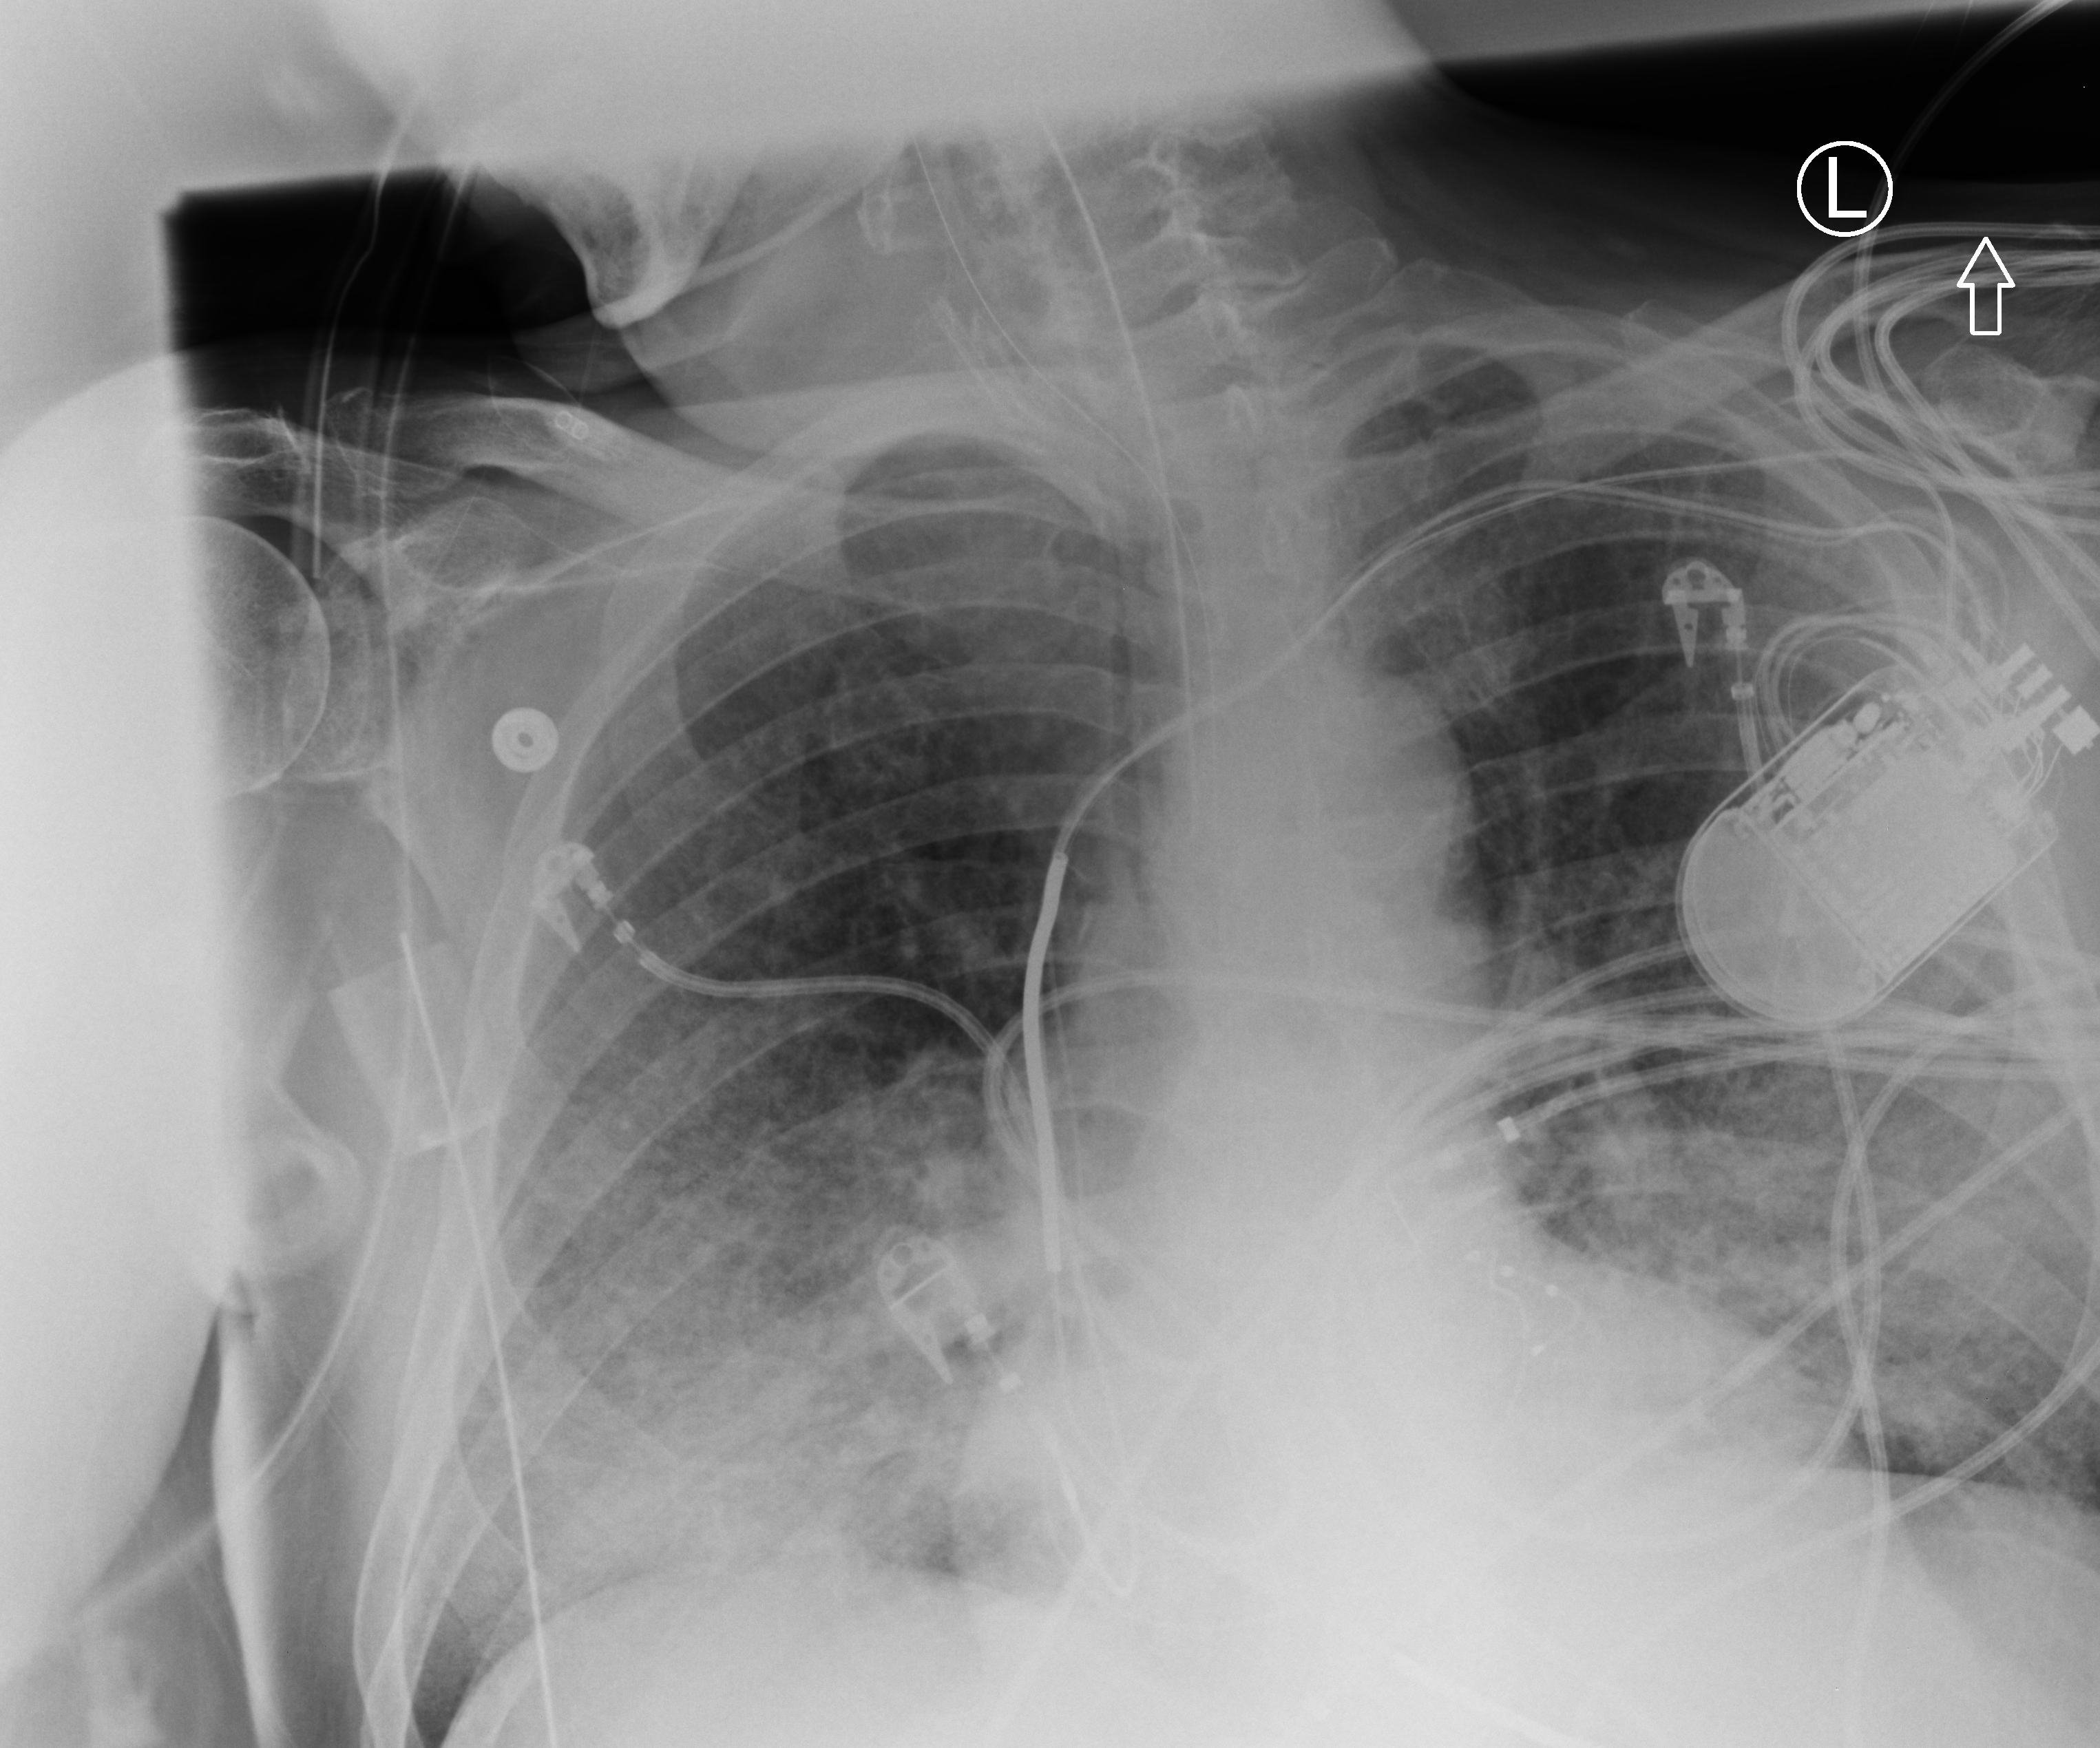
Chest X-ray (portable); anteroposterior (AP) projection. Patient hospitalised with COVID-19; male, aged 60–74 years.
Admission-level facts for this patient (not findings on this image; timing relative to this image not recorded):
- other chronic lung disease (admission record): no
- length of hospital stay: 36 days
- mechanically ventilated during this hospital stay: yes